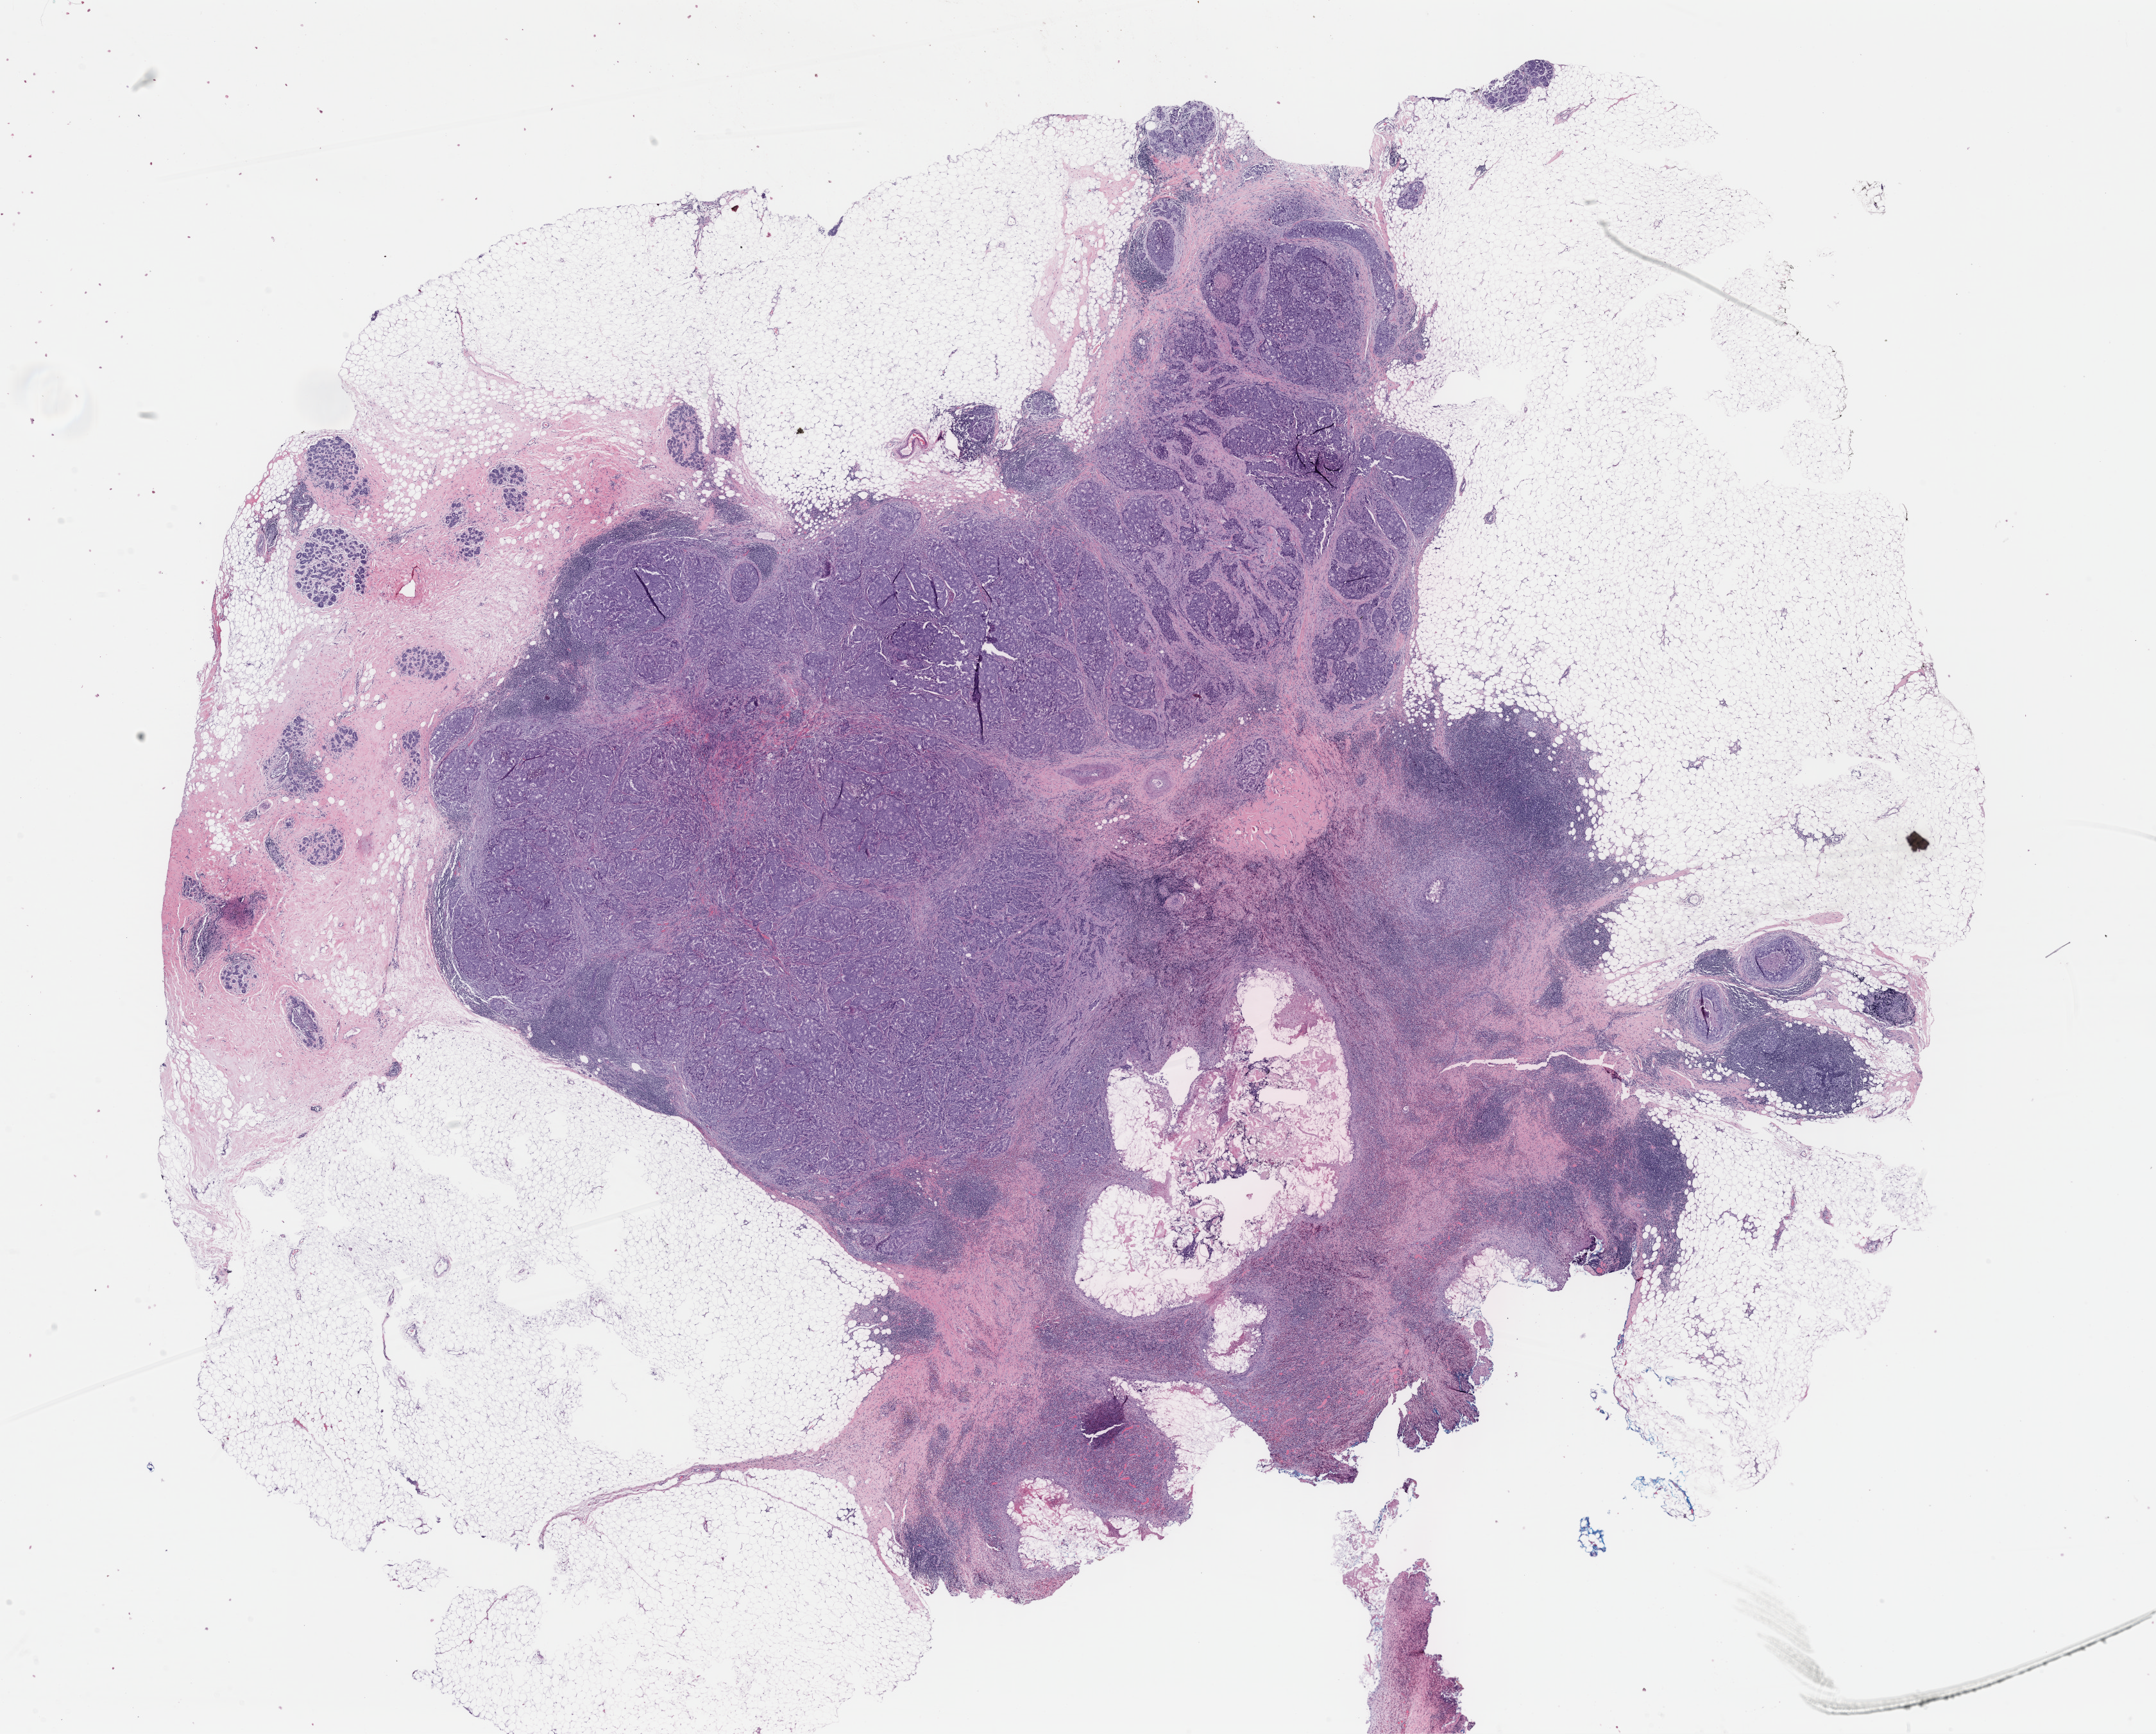
Digitized H&E-stained tissue section (whole slide), shown as a low-resolution overview of the whole scanned area (about 26.4 x 21.2 mm, from a 40x scan); formalin-fixed paraffin-embedded (FFPE) diagnostic section; primary tumour sample from the breast. Female patient; age at initial diagnosis 46 years.
AJCC pathologic stage: I (6th edition). Lymph nodes positive (case pathology): 0 of 3 examined. Pathologic diagnosis: Infiltrating duct carcinoma, NOS.